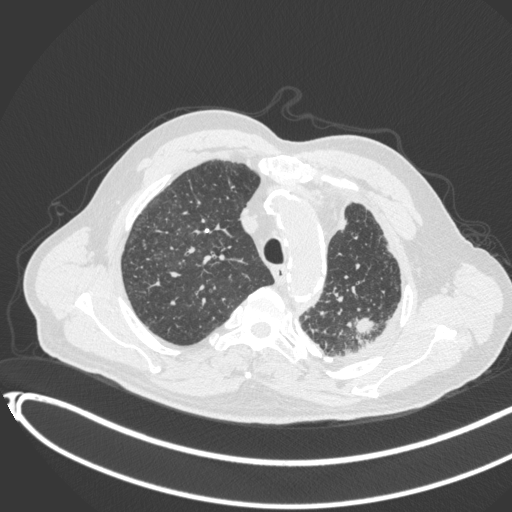
Chest CT, one axial slice; slice 337 of 451 in the series (ordered by position); 120 kVp; lung window (W 1500 / L -600 HU); 1 mm slice thickness; 512 × 512 image matrix, field of view 400 × 400 mm. Male patient, age 78 years. Case-level facts recorded for this patient, not image findings: clinical TNM (as recorded): T1c N0 M1.
Outlined on this slice (bounding box drawn by a radiologist):
- lung tumour (recorded histology: adenocarcinoma): bounding box [x1, y1, x2, y2] px = [346, 312, 382, 341]